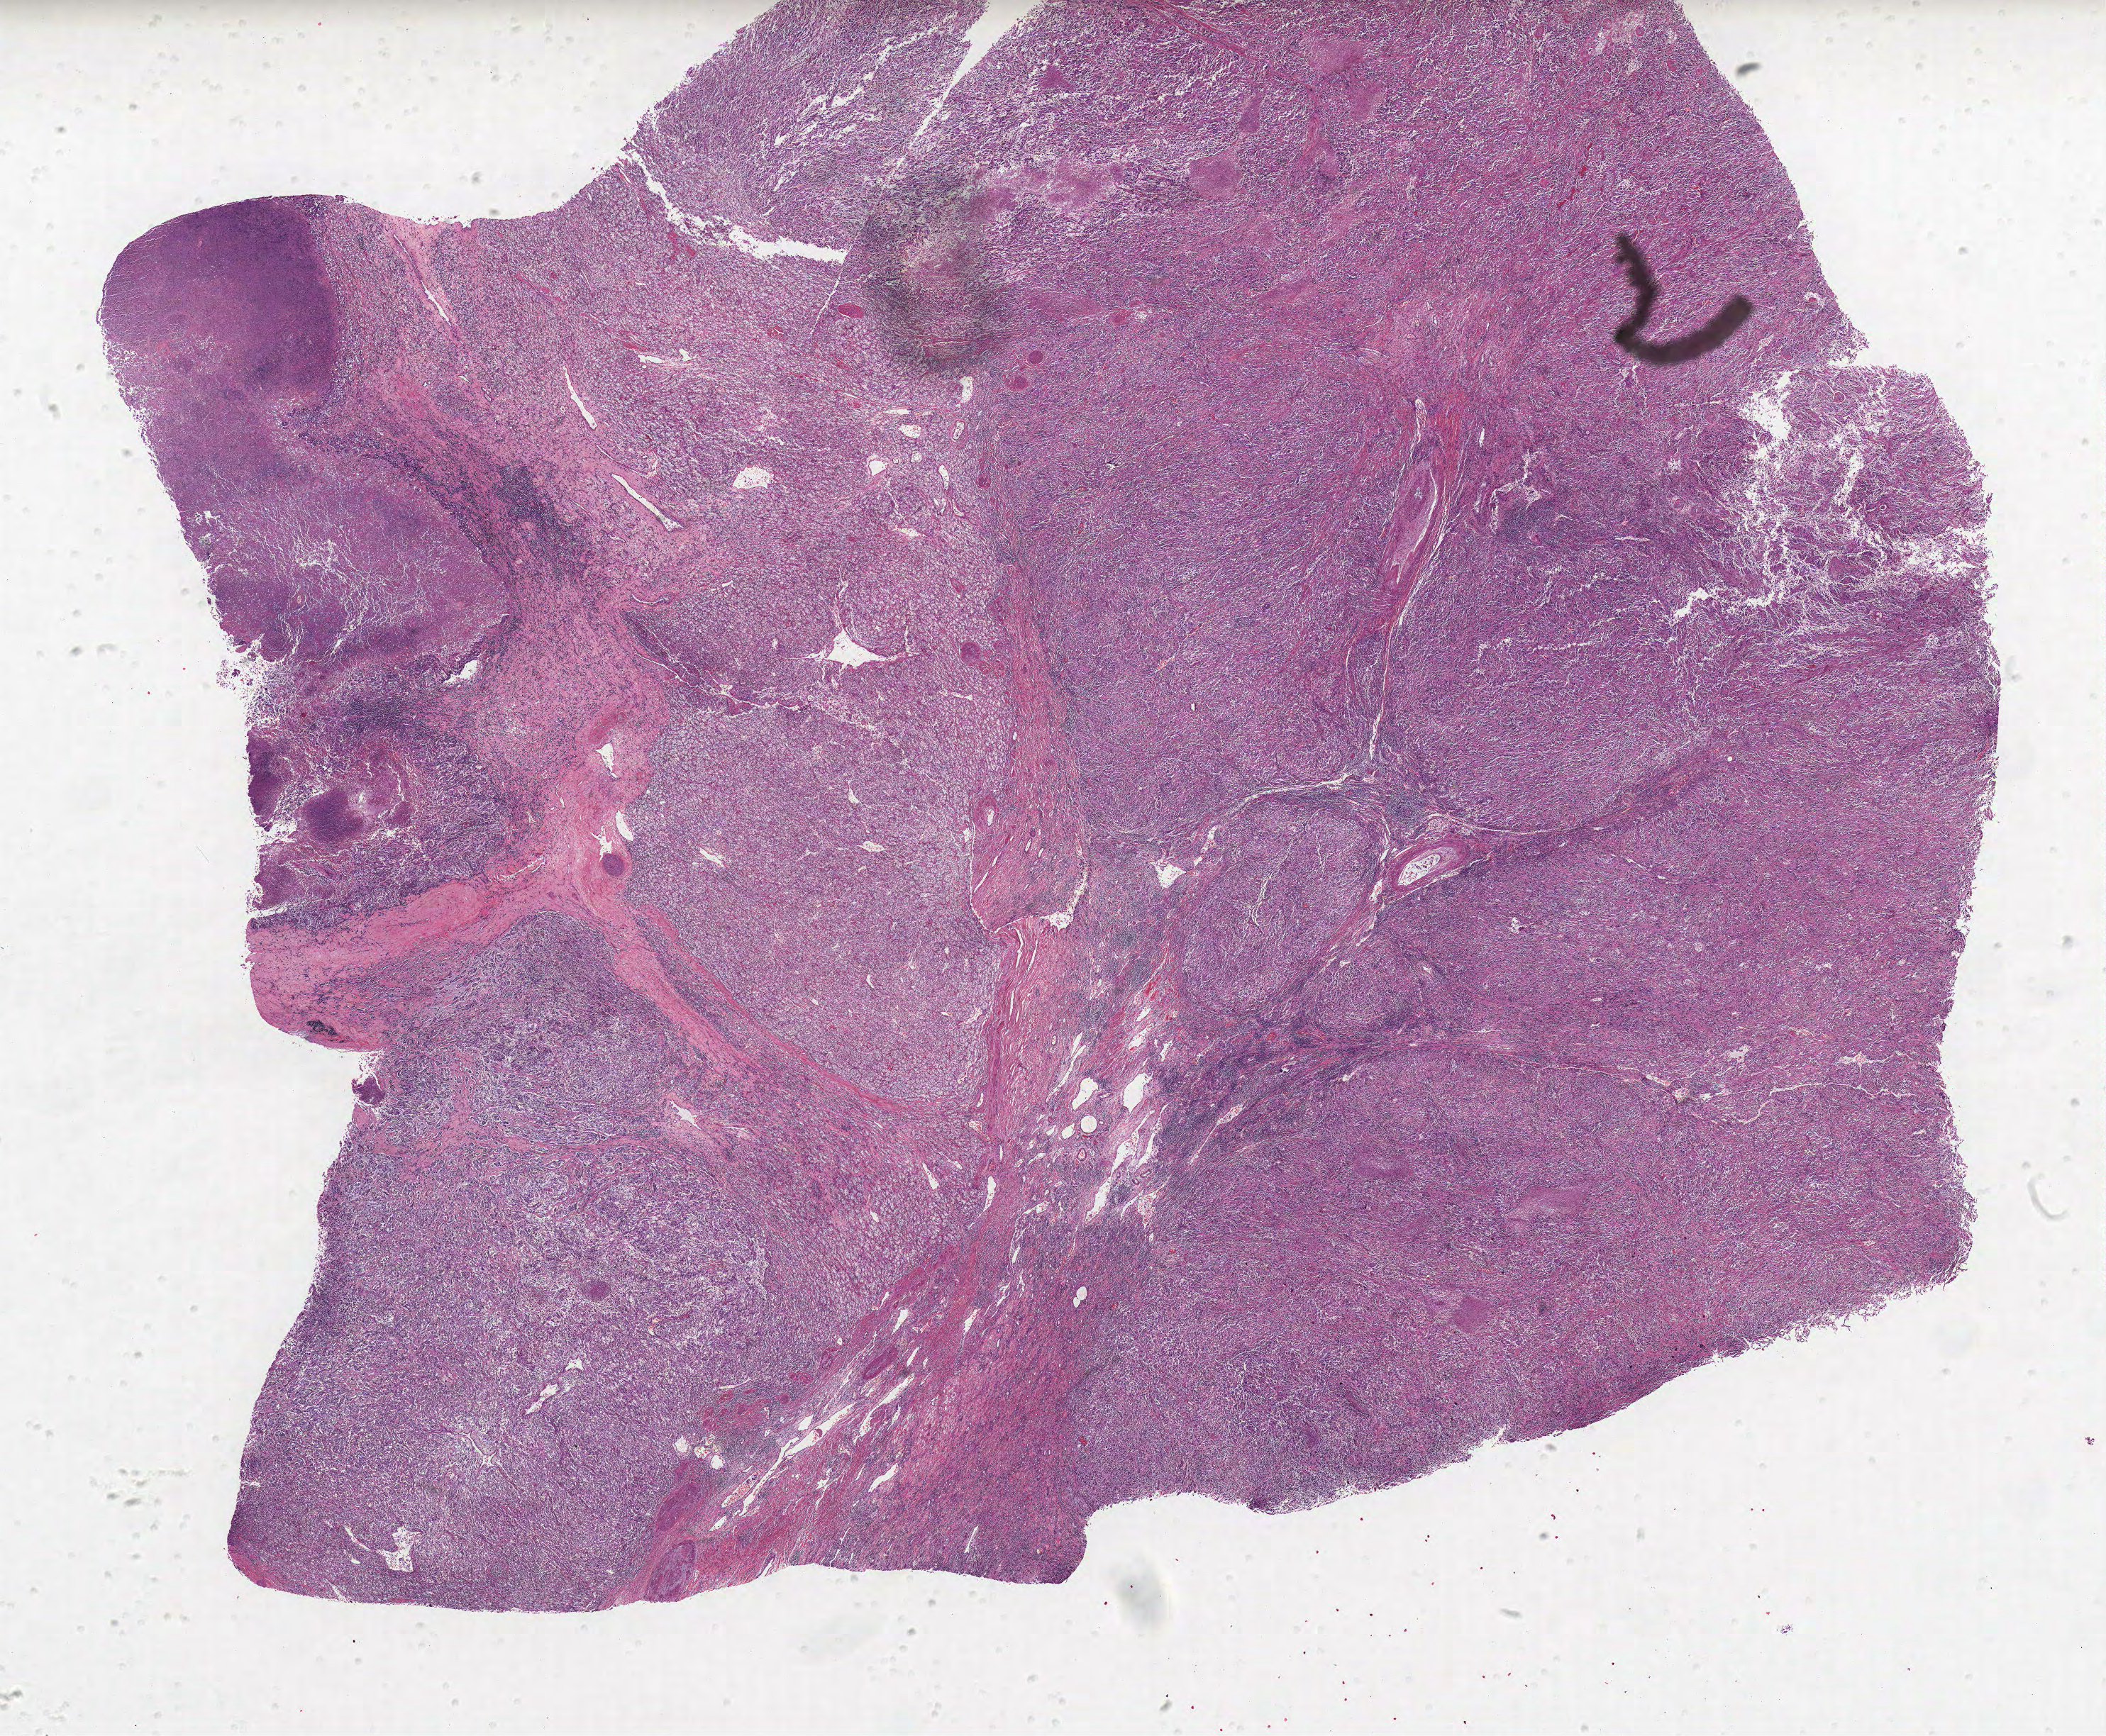
Whole-slide histology image, Hematoxylin and eosin (H&E) stained — low-resolution overview of the scanned area, about 23.7 x 19.6 mm, formalin-fixed paraffin-embedded (FFPE) diagnostic section, kidney, primary tumour sample. Patient: female, age at initial diagnosis 74 years. Histologic grade: G4 (undifferentiated).
* laterality: right
* histologic diagnosis: Clear cell adenocarcinoma, NOS
* AJCC pathologic stage: IV